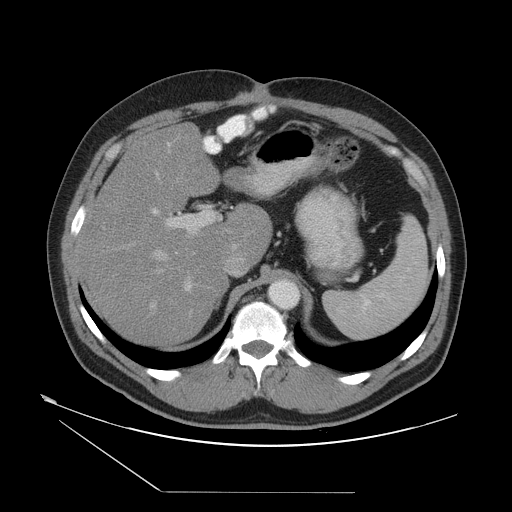
Contrast-enhanced abdominal CT, one axial slice. Slice 33 of 55 in the series (ordered by position). 120 kVp. Intravenous contrast given. Soft-tissue window (W 400 / L 40 HU). 512 × 512 image matrix, field of view 454 × 454 mm. Male patient, age 59 years. From the clinical record (not read from this slice): diagnosis: colorectal cancer liver metastases, imaged before liver resection; multiple liver metastases: yes; largest metastasis: 0.3 cm.
Structures marked on this image (manually delineated by an expert):
- hepatic veins: box from (x=150, y=139) to (x=189, y=315) px
- liver: (x=82, y=127)–(x=271, y=345)
- planned liver remnant (the part of the liver to remain after resection): (x=81, y=144)–(x=271, y=345)
- portal vein (with intrahepatic branches): (x=152, y=143)–(x=230, y=315)